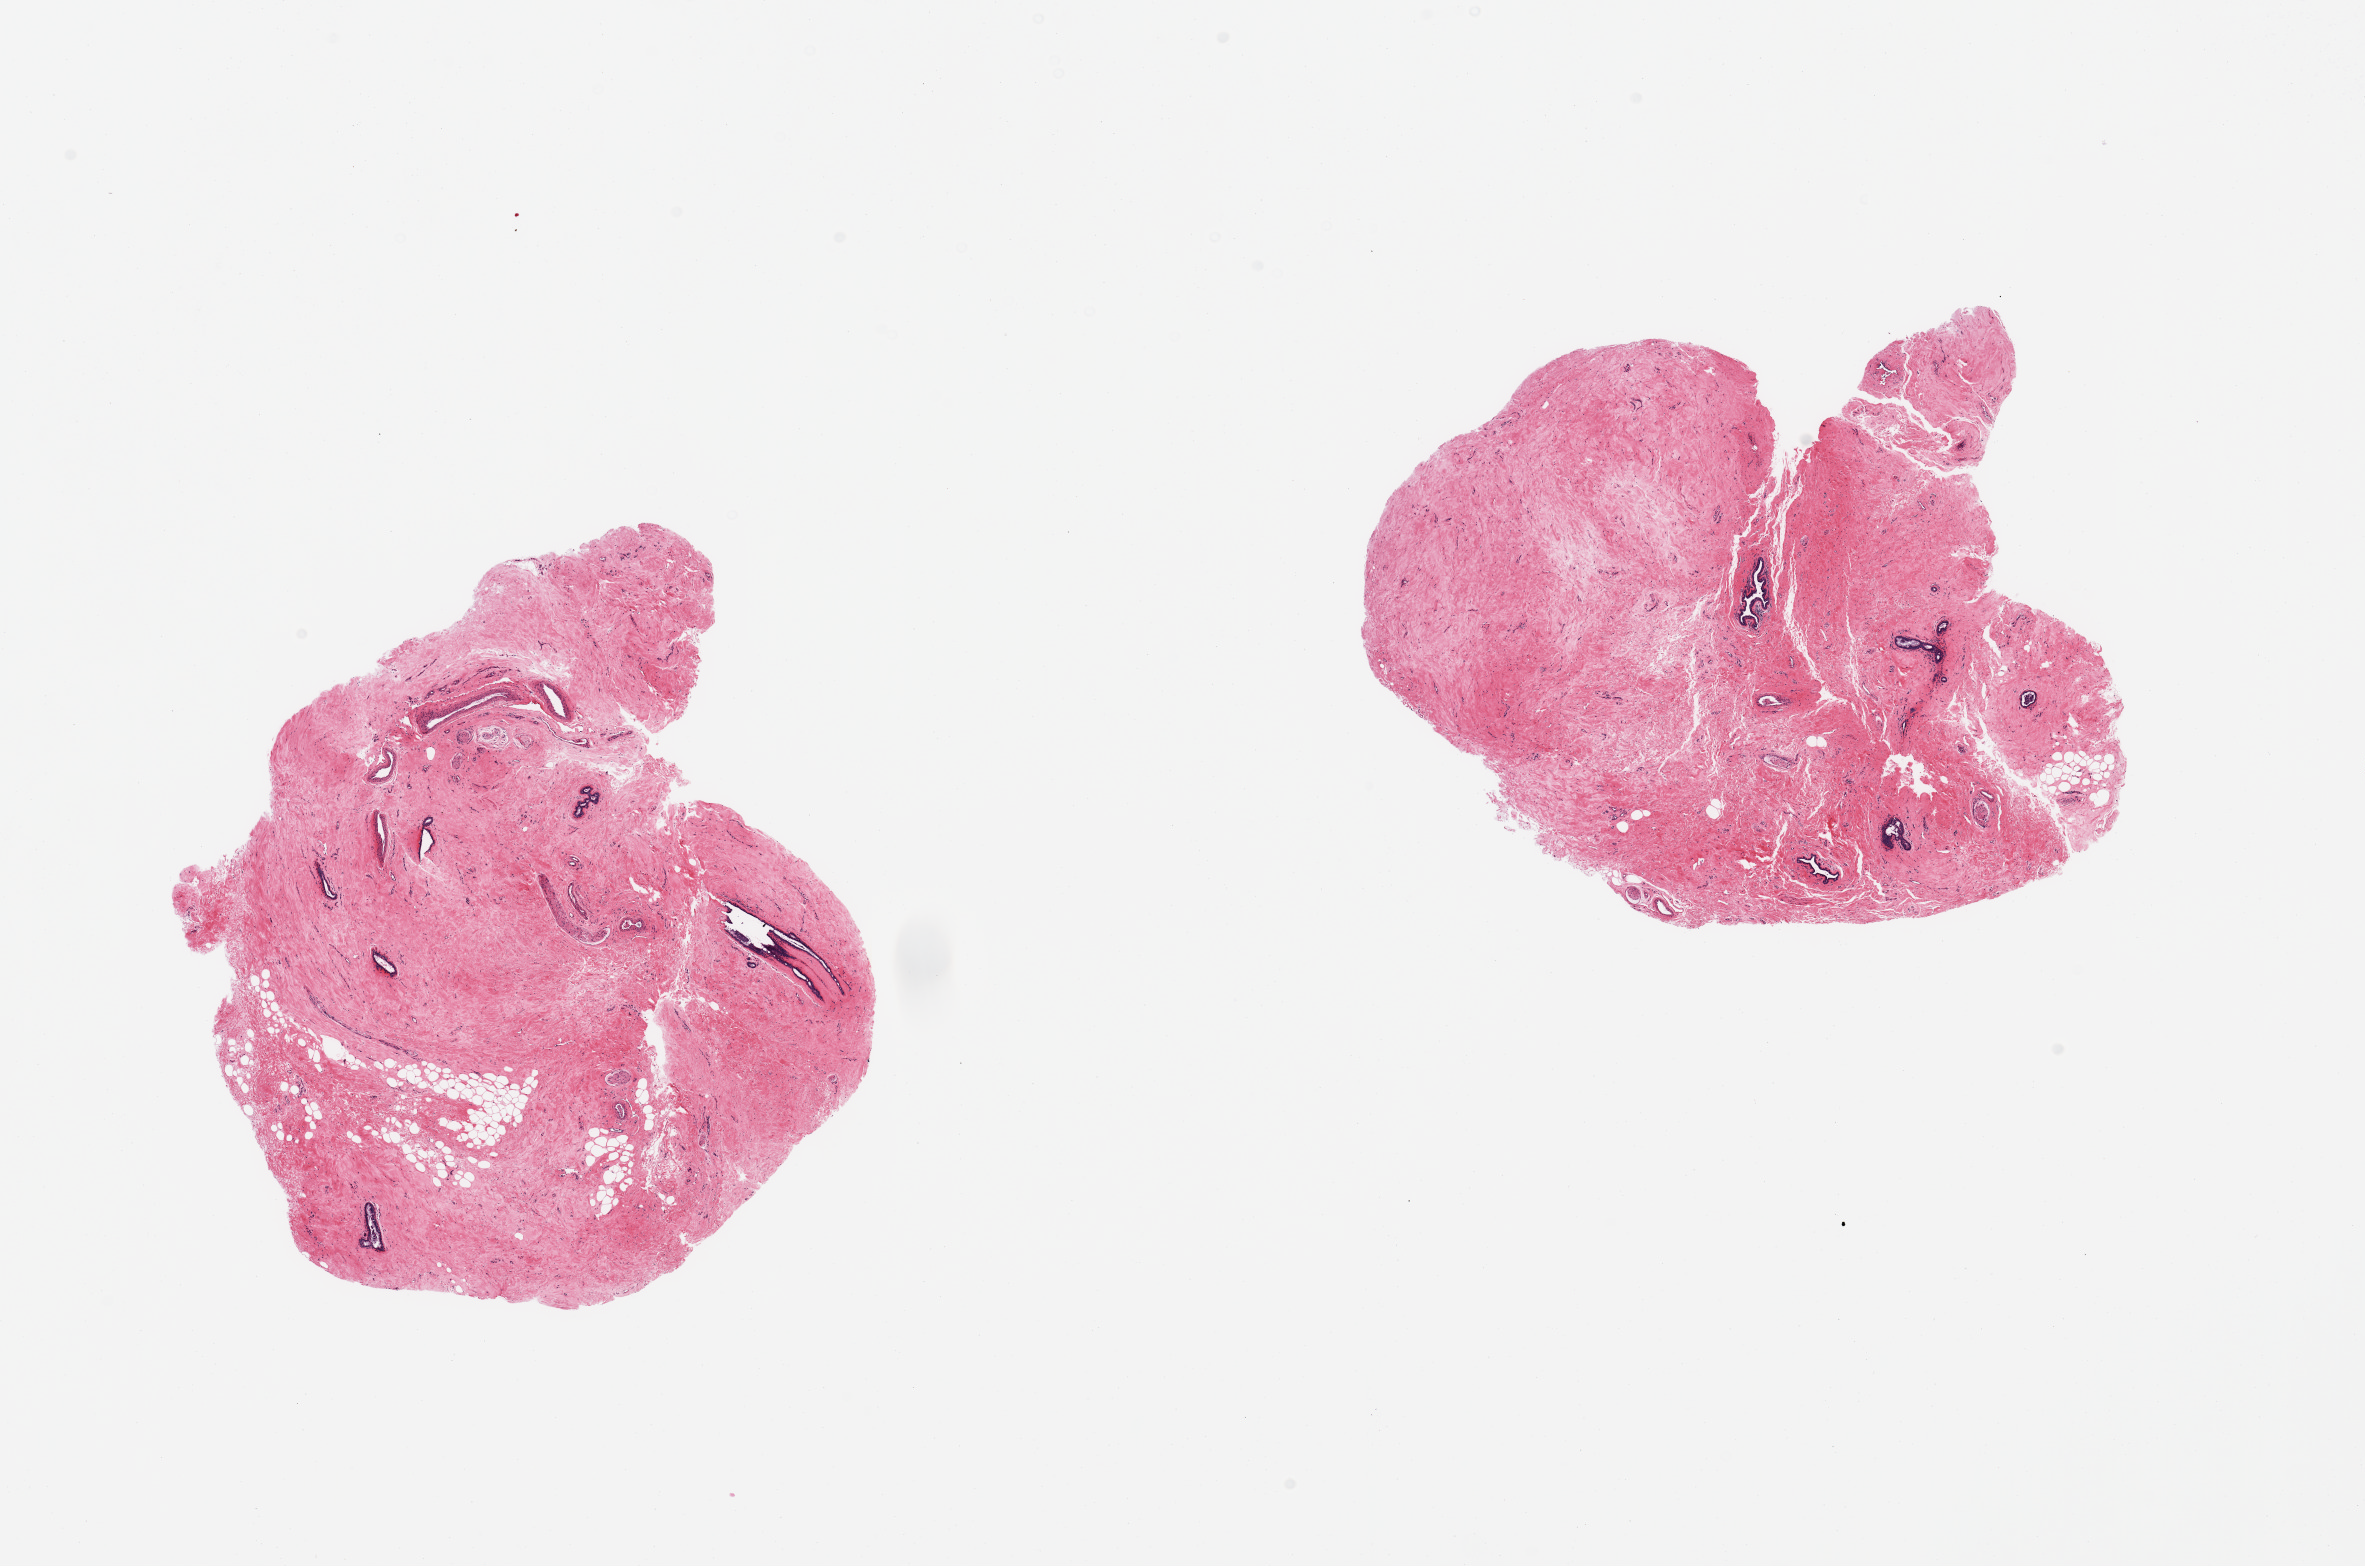
Digitized H&E-stained section, low-resolution overview of the scanned area, about 18.7 x 12.4 mm (acquisition: 20x scan). PAXgene-fixed, paraffin-embedded tissue. Sampled site (target tissue): breast. Donor tissue sample. Male donor.
• reviewer comment on this tissue sample: 2 pieces; gynecomastoid stromal and ductal hyperplasia